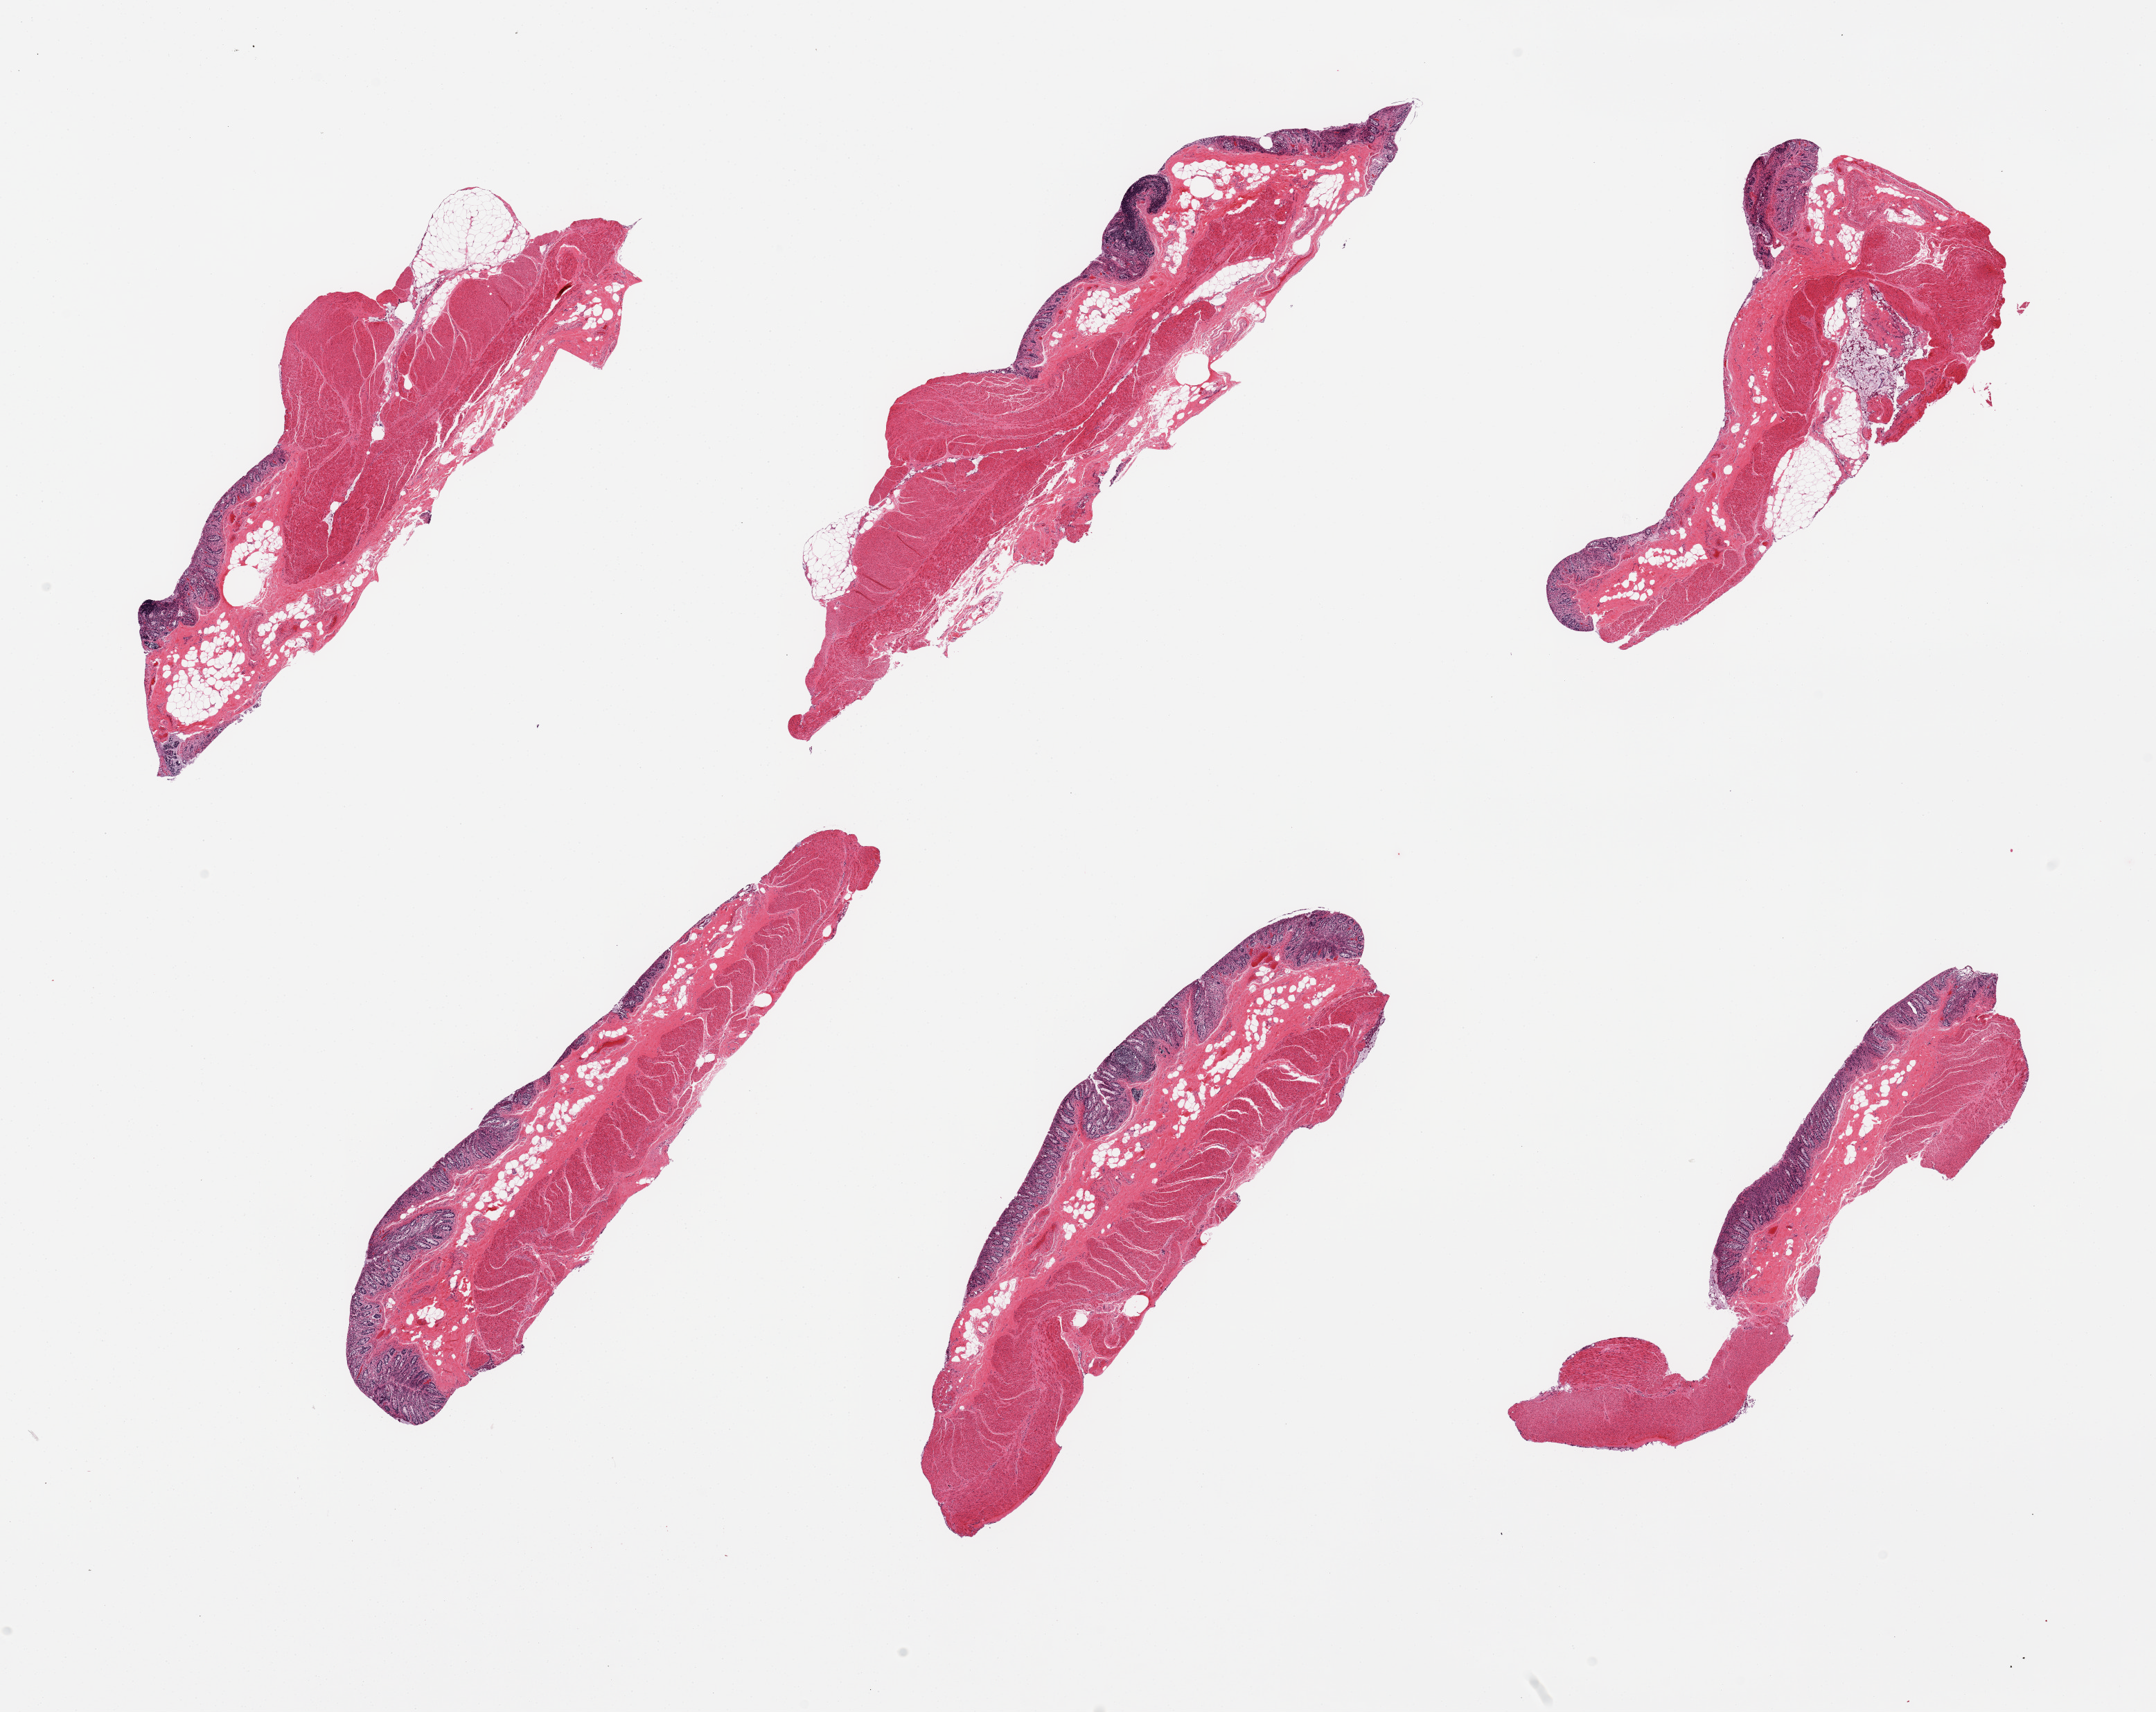
H&E whole-slide image — shown as a low-resolution overview of the whole scanned area (about 24.6 x 19.5 mm); PAXgene-fixed paraffin-embedded (PFPE) section; section of transverse colon (target tissue); donor tissue sample. Male donor.
* reviewer comment on this tissue sample: 6 pieces, severely autolyzed mucosa and muscularis